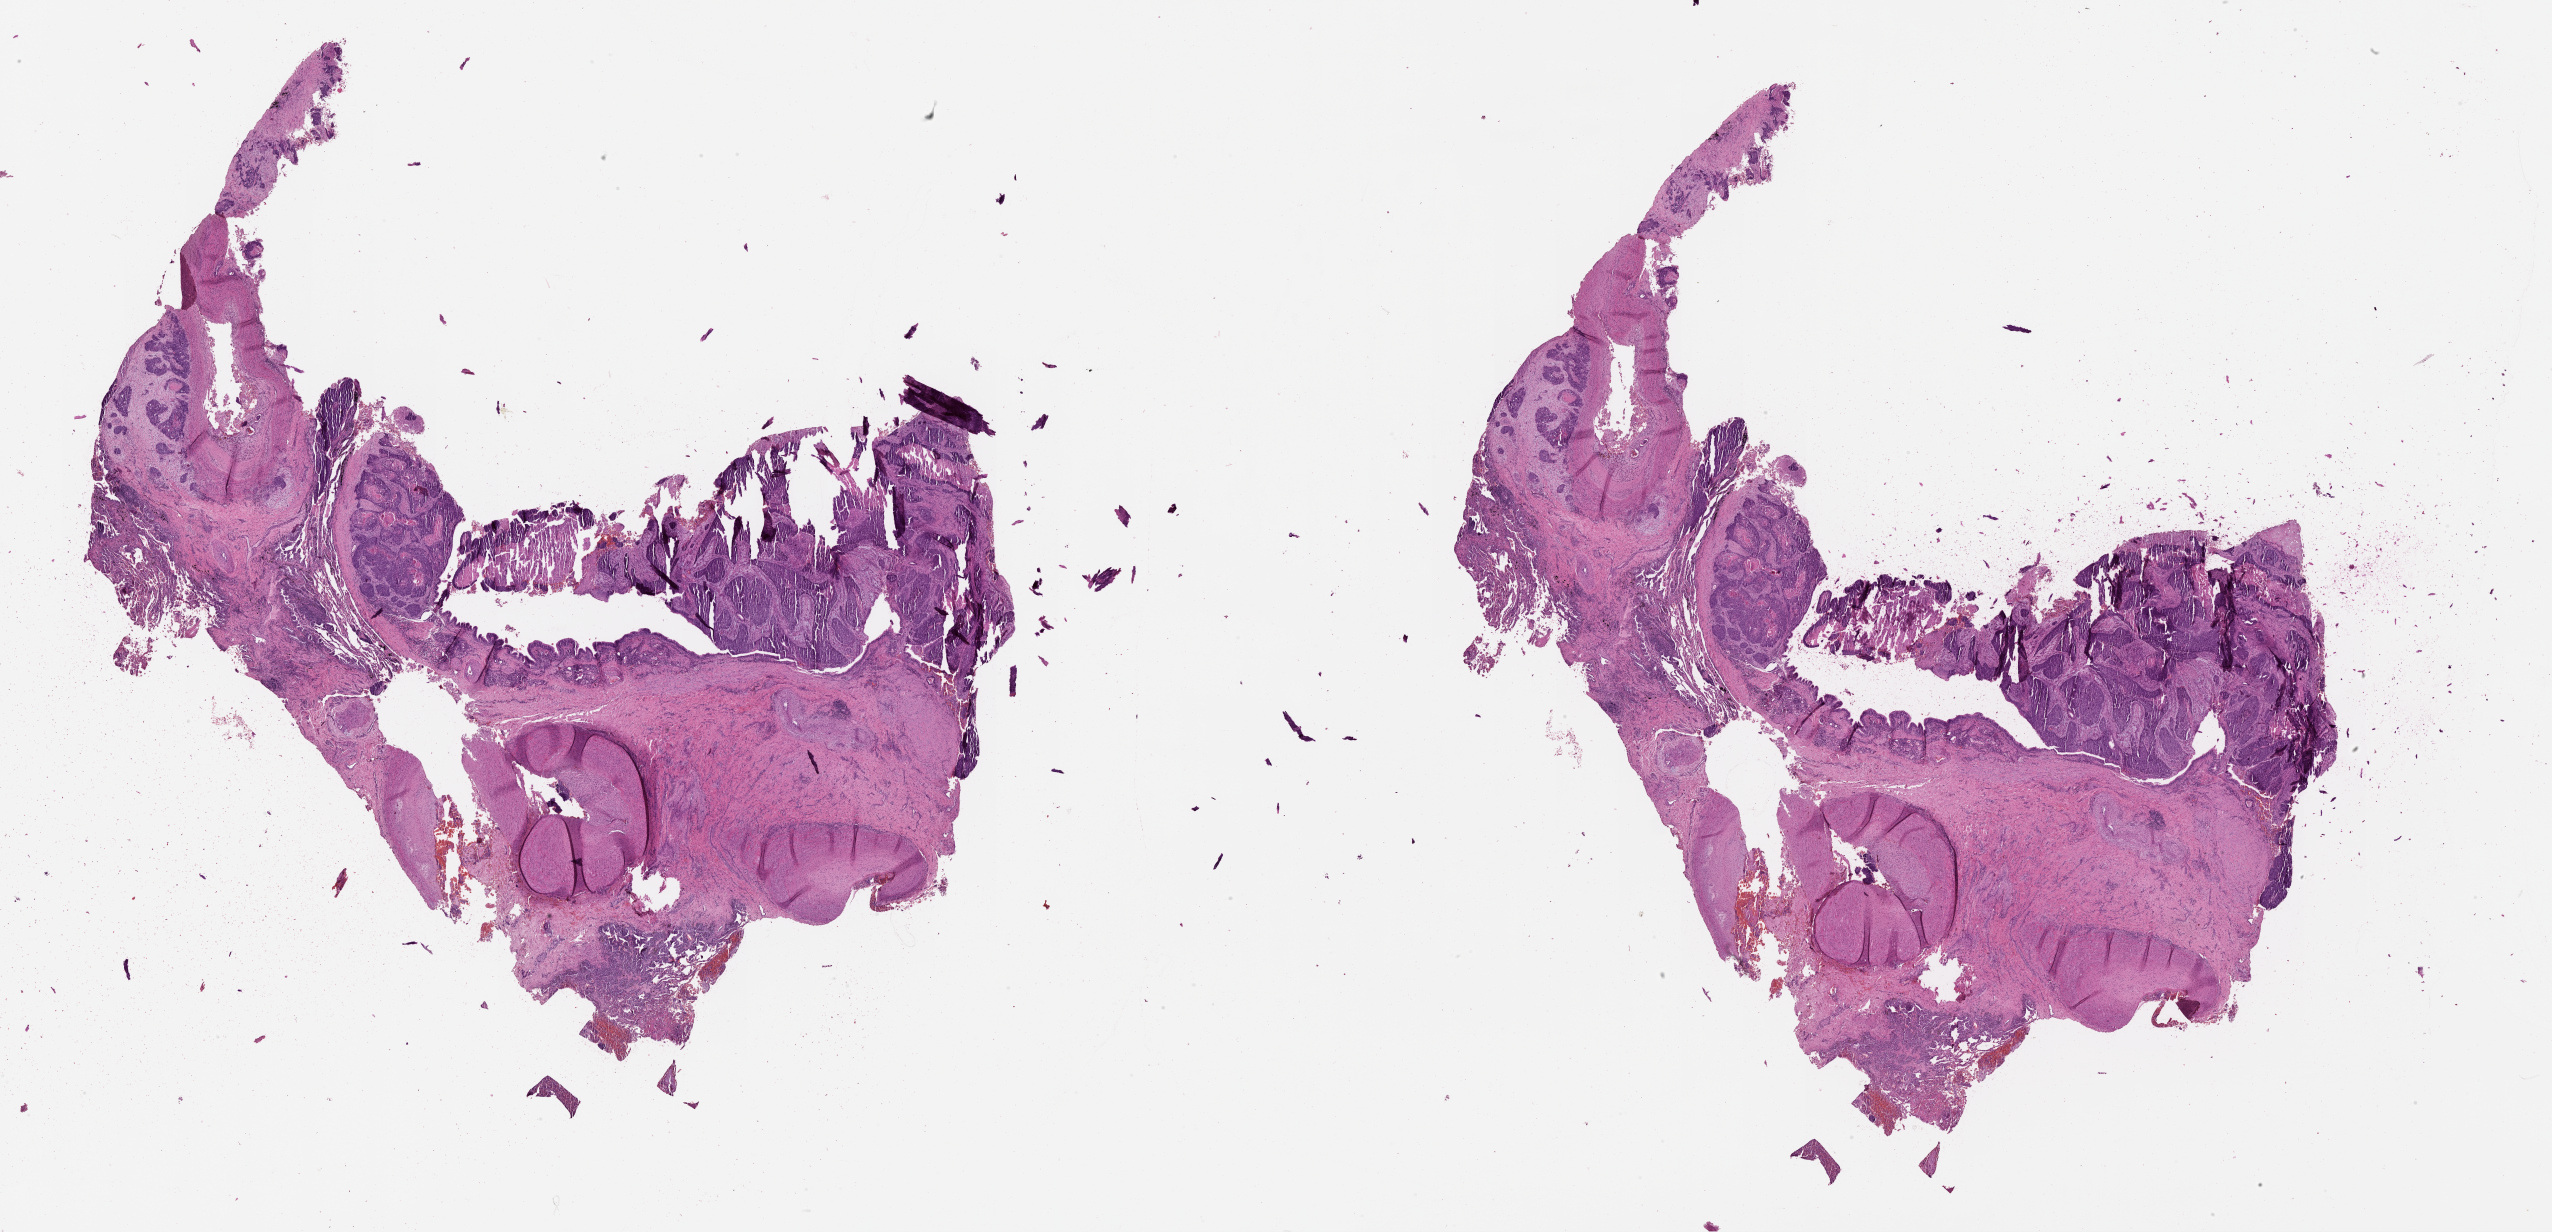
Whole-slide histology image, Hematoxylin and eosin (H&E) stained, whole scanned area (about 41.1 x 19.8 mm, slide scanned at 20x) shown as a low-resolution overview; lung, tumour tissue. 59-year-old male patient.
- patient diagnosis (cohort enrolment): squamous cell carcinoma (lung)